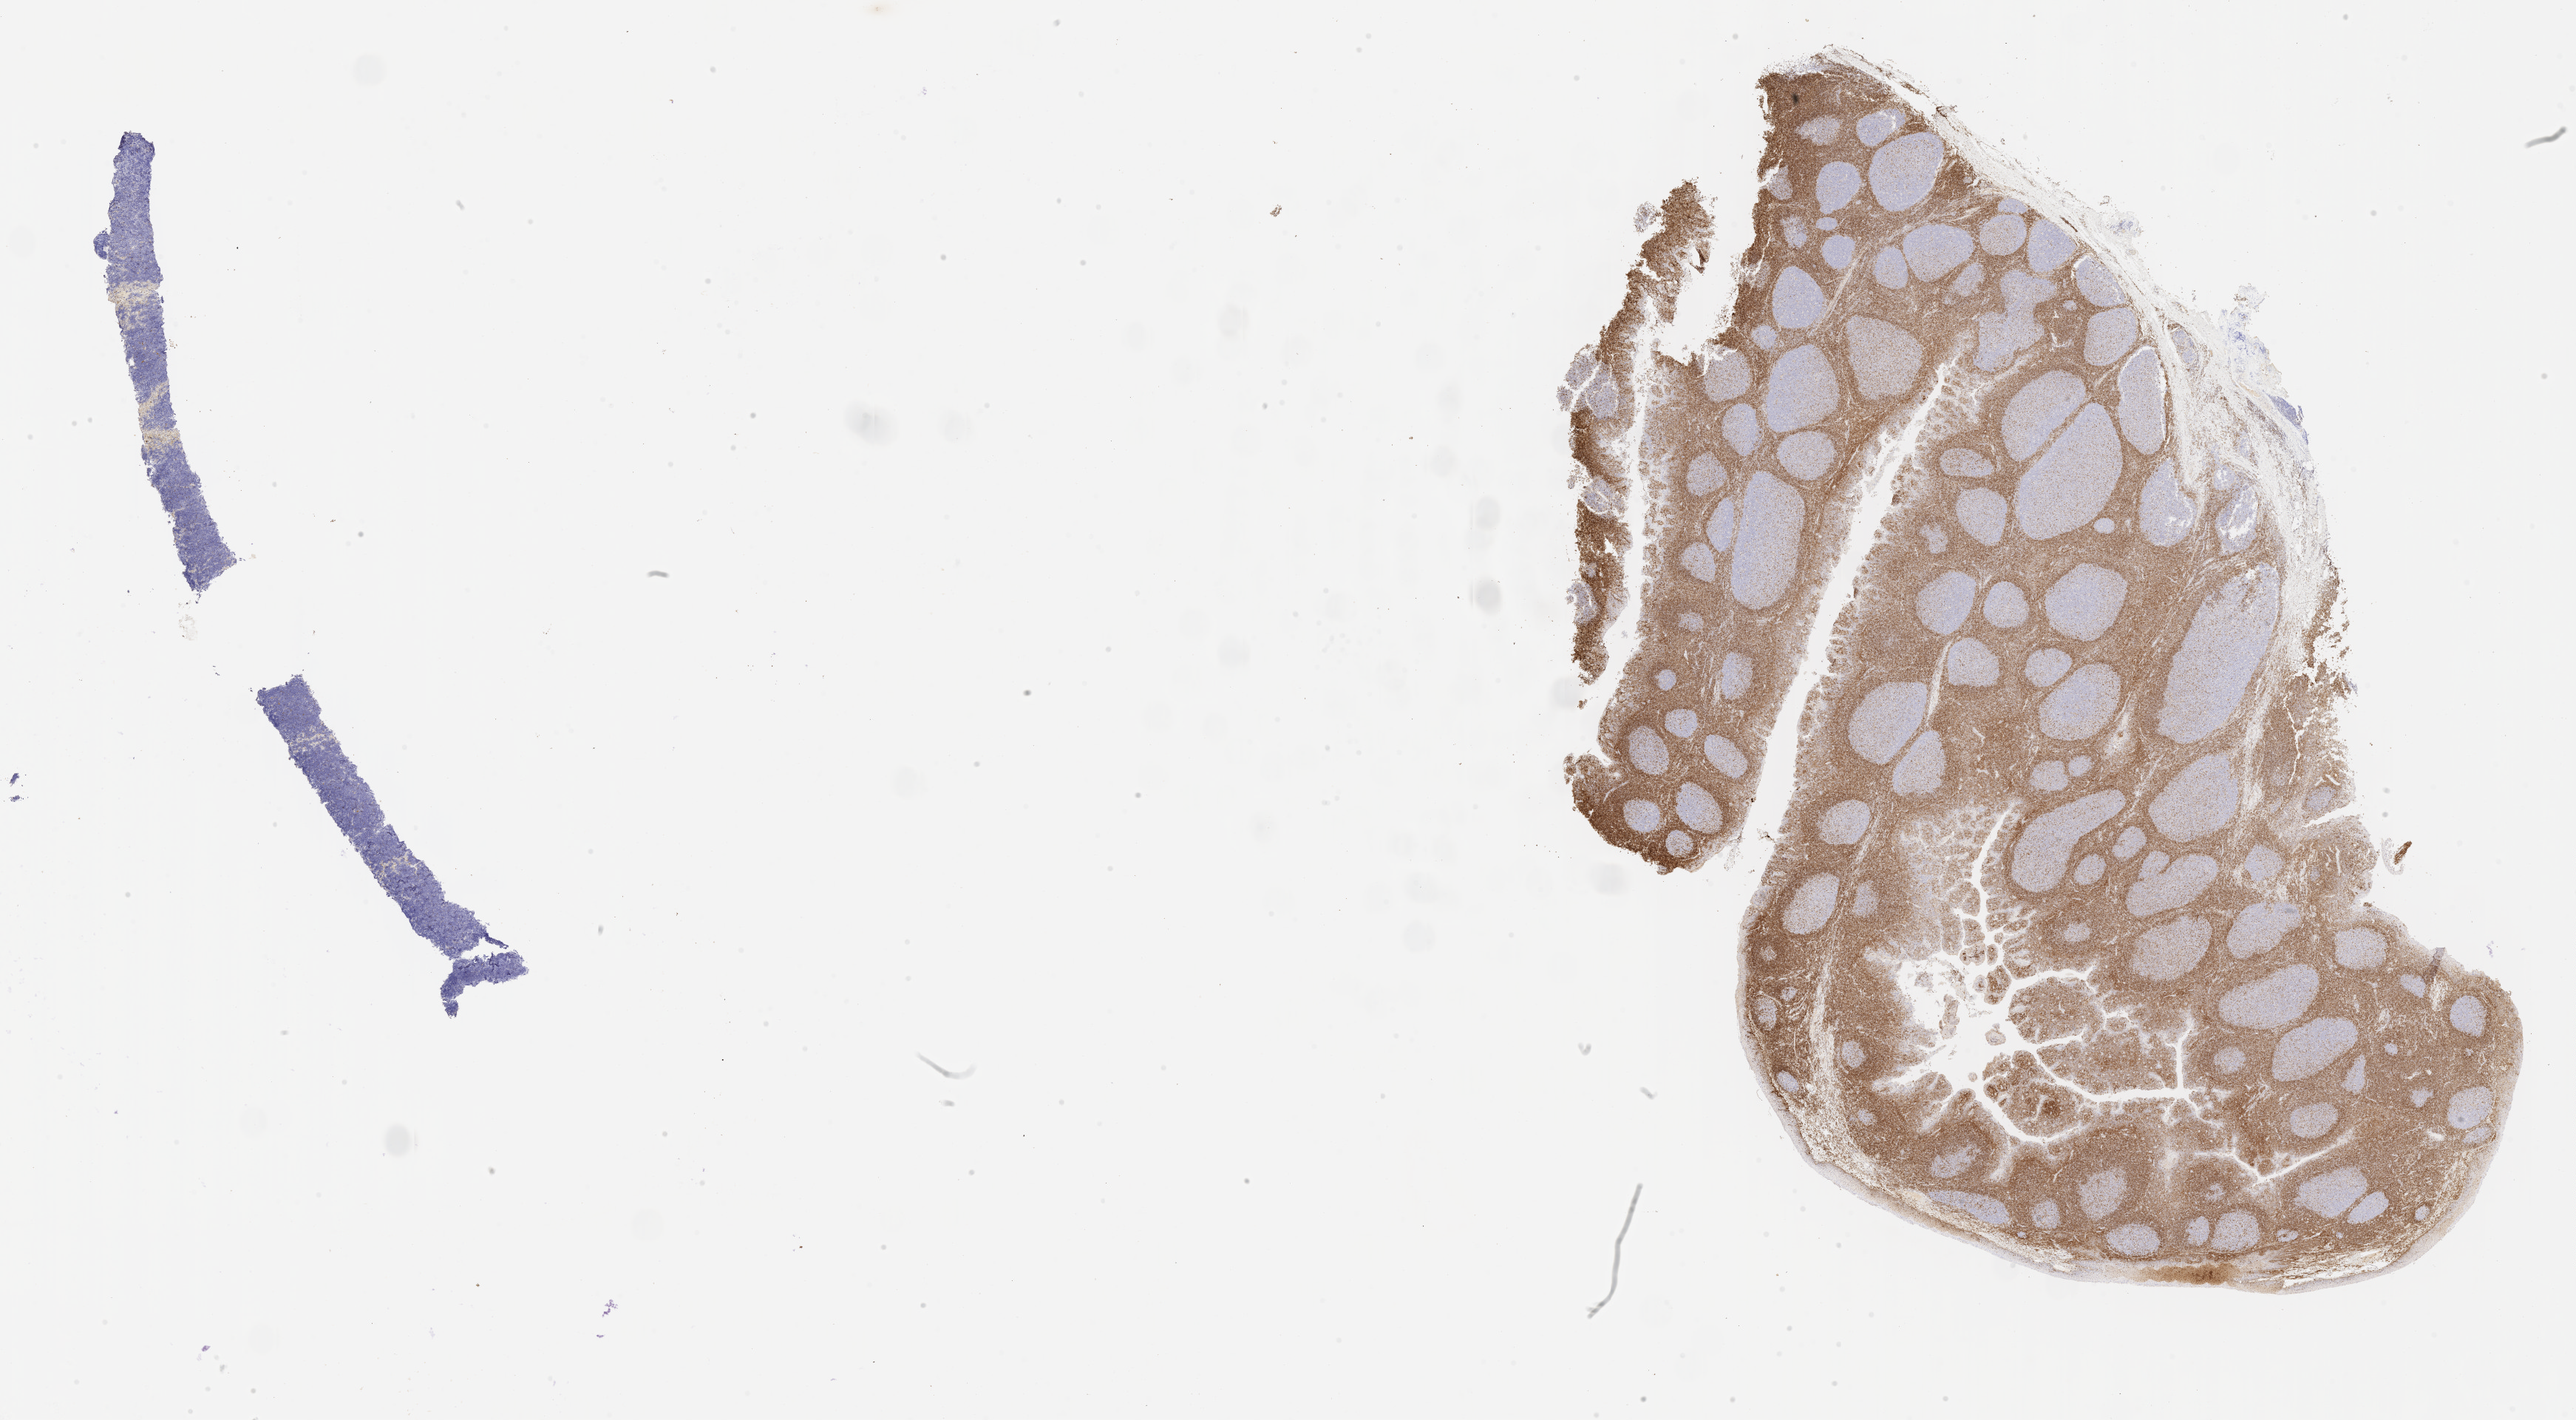
Immunohistochemistry (IHC) whole-slide image stained for BCL2 — low-resolution overview of the scanned area, about 28.2 x 15.5 mm. Patient sex: female.
Specimen: tumor tissue.